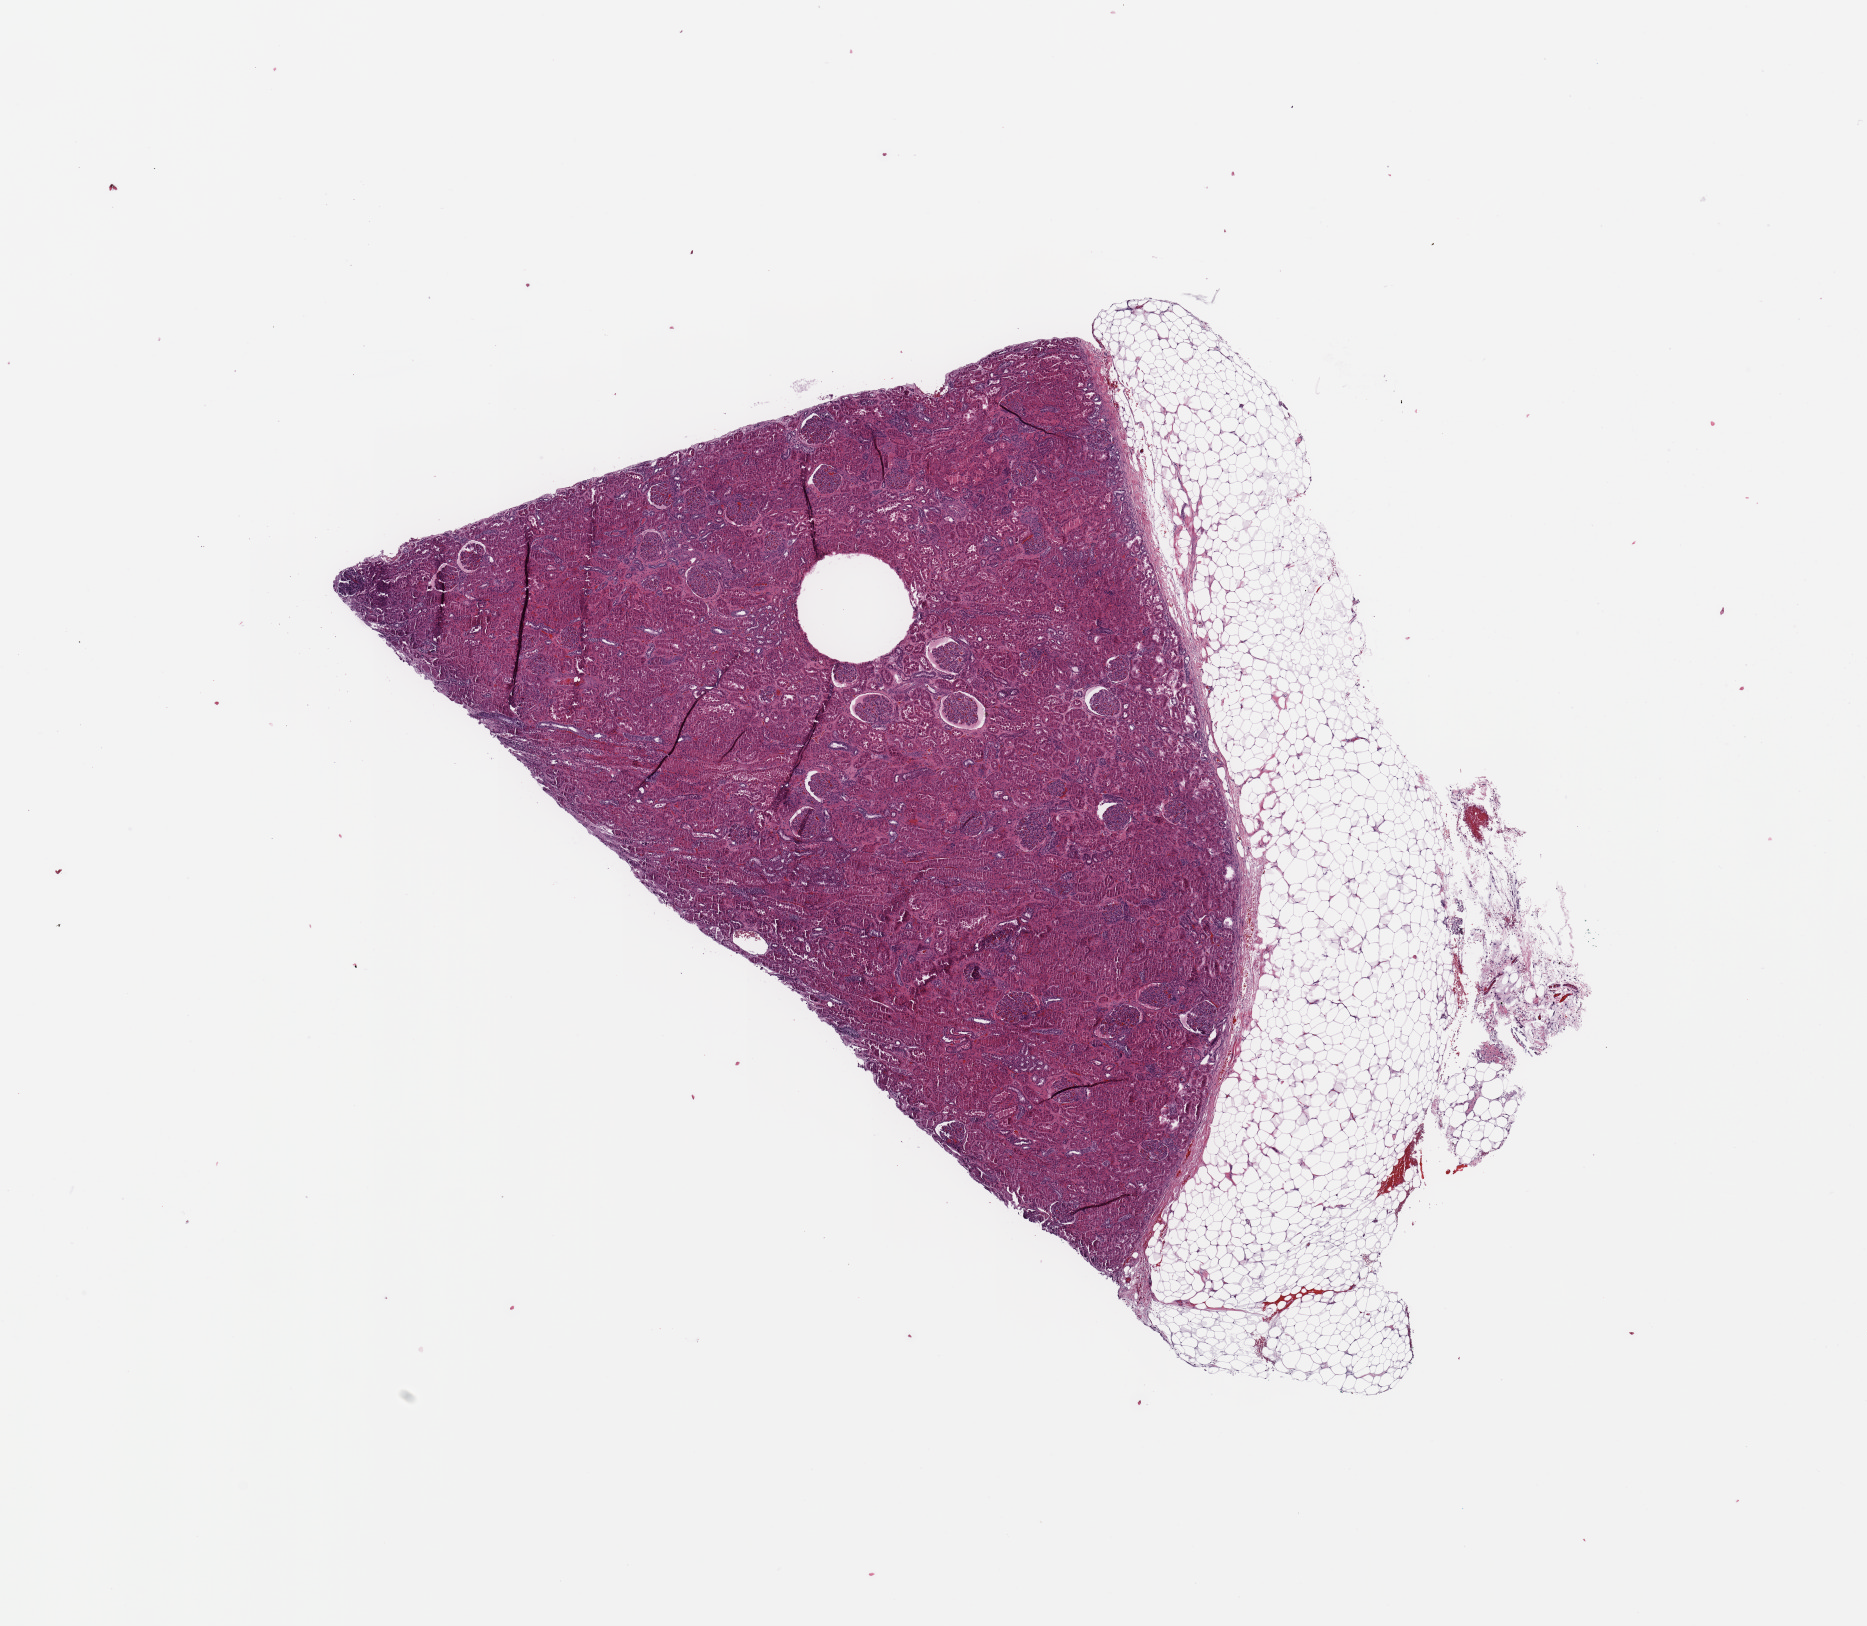
Digitized H&E tissue section (whole slide) — low-resolution overview of the scanned area, about 14.8 x 12.9 mm; normal (non-tumour) tissue sample, sampled site: kidney. Patient: male, age 53 years.
* this section: normal (non-tumour) tissue from the same patient
* patient diagnosis: Renal cell carcinoma, NOS